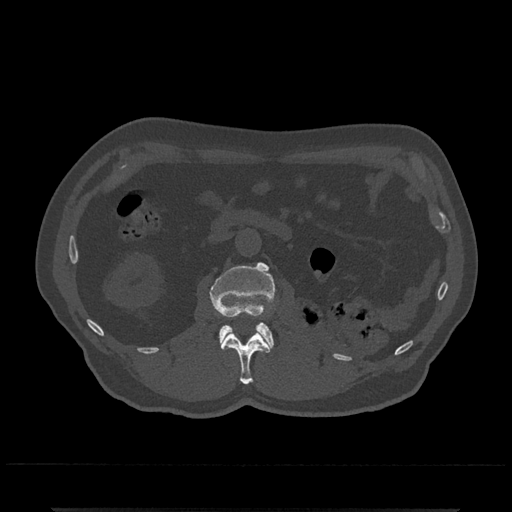
CT including the spine, one axial slice; slice 326 of 797 in the series (ordered by position); bone window (W 1800 / L 400 HU); 0.5 mm slice thickness; 512 × 512 image matrix. Patient: male, 67 years. Case-level facts recorded for this patient, not image findings: primary cancer: prostate.
Annotated regions visible in this slice (semi-automatic segmentation, software-assisted and operator-edited):
- L1 vertebra: bounding box [x1, y1, x2, y2] px = [221, 331, 270, 385]
- L2 vertebra: [210, 262, 276, 351]